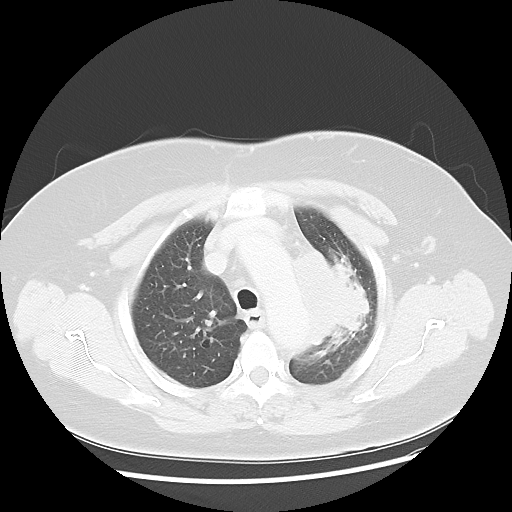
Chest CT, one axial slice. Position 37 of 49 along the scan axis. Reconstruction kernel LUNG. 120 kVp. Lung window (W 1500 / L -600 HU). 5 mm slice thickness. 512 × 512 image matrix, field of view 374 × 374 mm. Female patient, age 58 years. Case-level facts recorded for this patient, not image findings: clinical TNM (as recorded): T4 N3 M0.
Annotated regions visible in this slice (rectangle marked by the reading radiologist):
- lung tumour (recorded histology: small cell carcinoma): box from (x=294, y=243) to (x=378, y=343) px